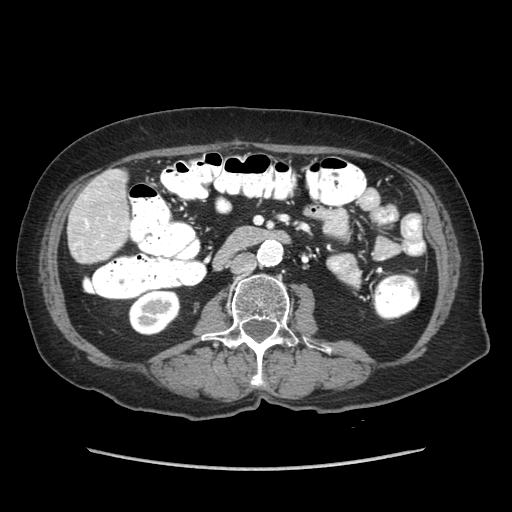
Contrast-enhanced abdominal CT (liver protocol), one axial slice; position 13 of 89 along the scan axis; reconstruction kernel STANDARD; 140 kVp; soft-tissue window (W 400 / L 40 HU); 2.5 mm slice thickness; 512 × 512 image matrix, field of view 360 × 360 mm. From the clinical record (not read from this slice): diagnosis: hepatocellular carcinoma (patient treated with transarterial chemoembolisation; whether this scan precedes or follows treatment is not stated here); TNM stage (as recorded): Stage-IIIA; Child-Pugh class: A; tumour differentiation: well differentiated; tumour size: 11 cm.
Structures marked on this image (semi-automatically segmented with operator editing):
- liver parenchyma outside the tumour (the mass and vessels are separate outlines, so this box may not span the whole liver): bounding box [x1, y1, x2, y2] px = [68, 170, 128, 262]
- liver vessels: [84, 218, 110, 236]